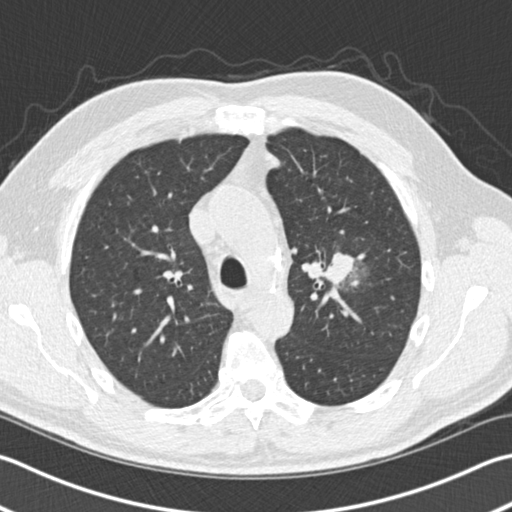
Low-dose screening chest CT, one axial slice; position 108 of 153 along the scan axis; lung window (W 1500 / L -600 HU); 2 mm slice thickness; 512 × 512 image matrix.
Structures marked on this image (outlined manually by an expert reader):
- lesion 1 (tumor, upper lobe of left lung): bounding box <325,253,353,286> (left, top, right, bottom; pixels)